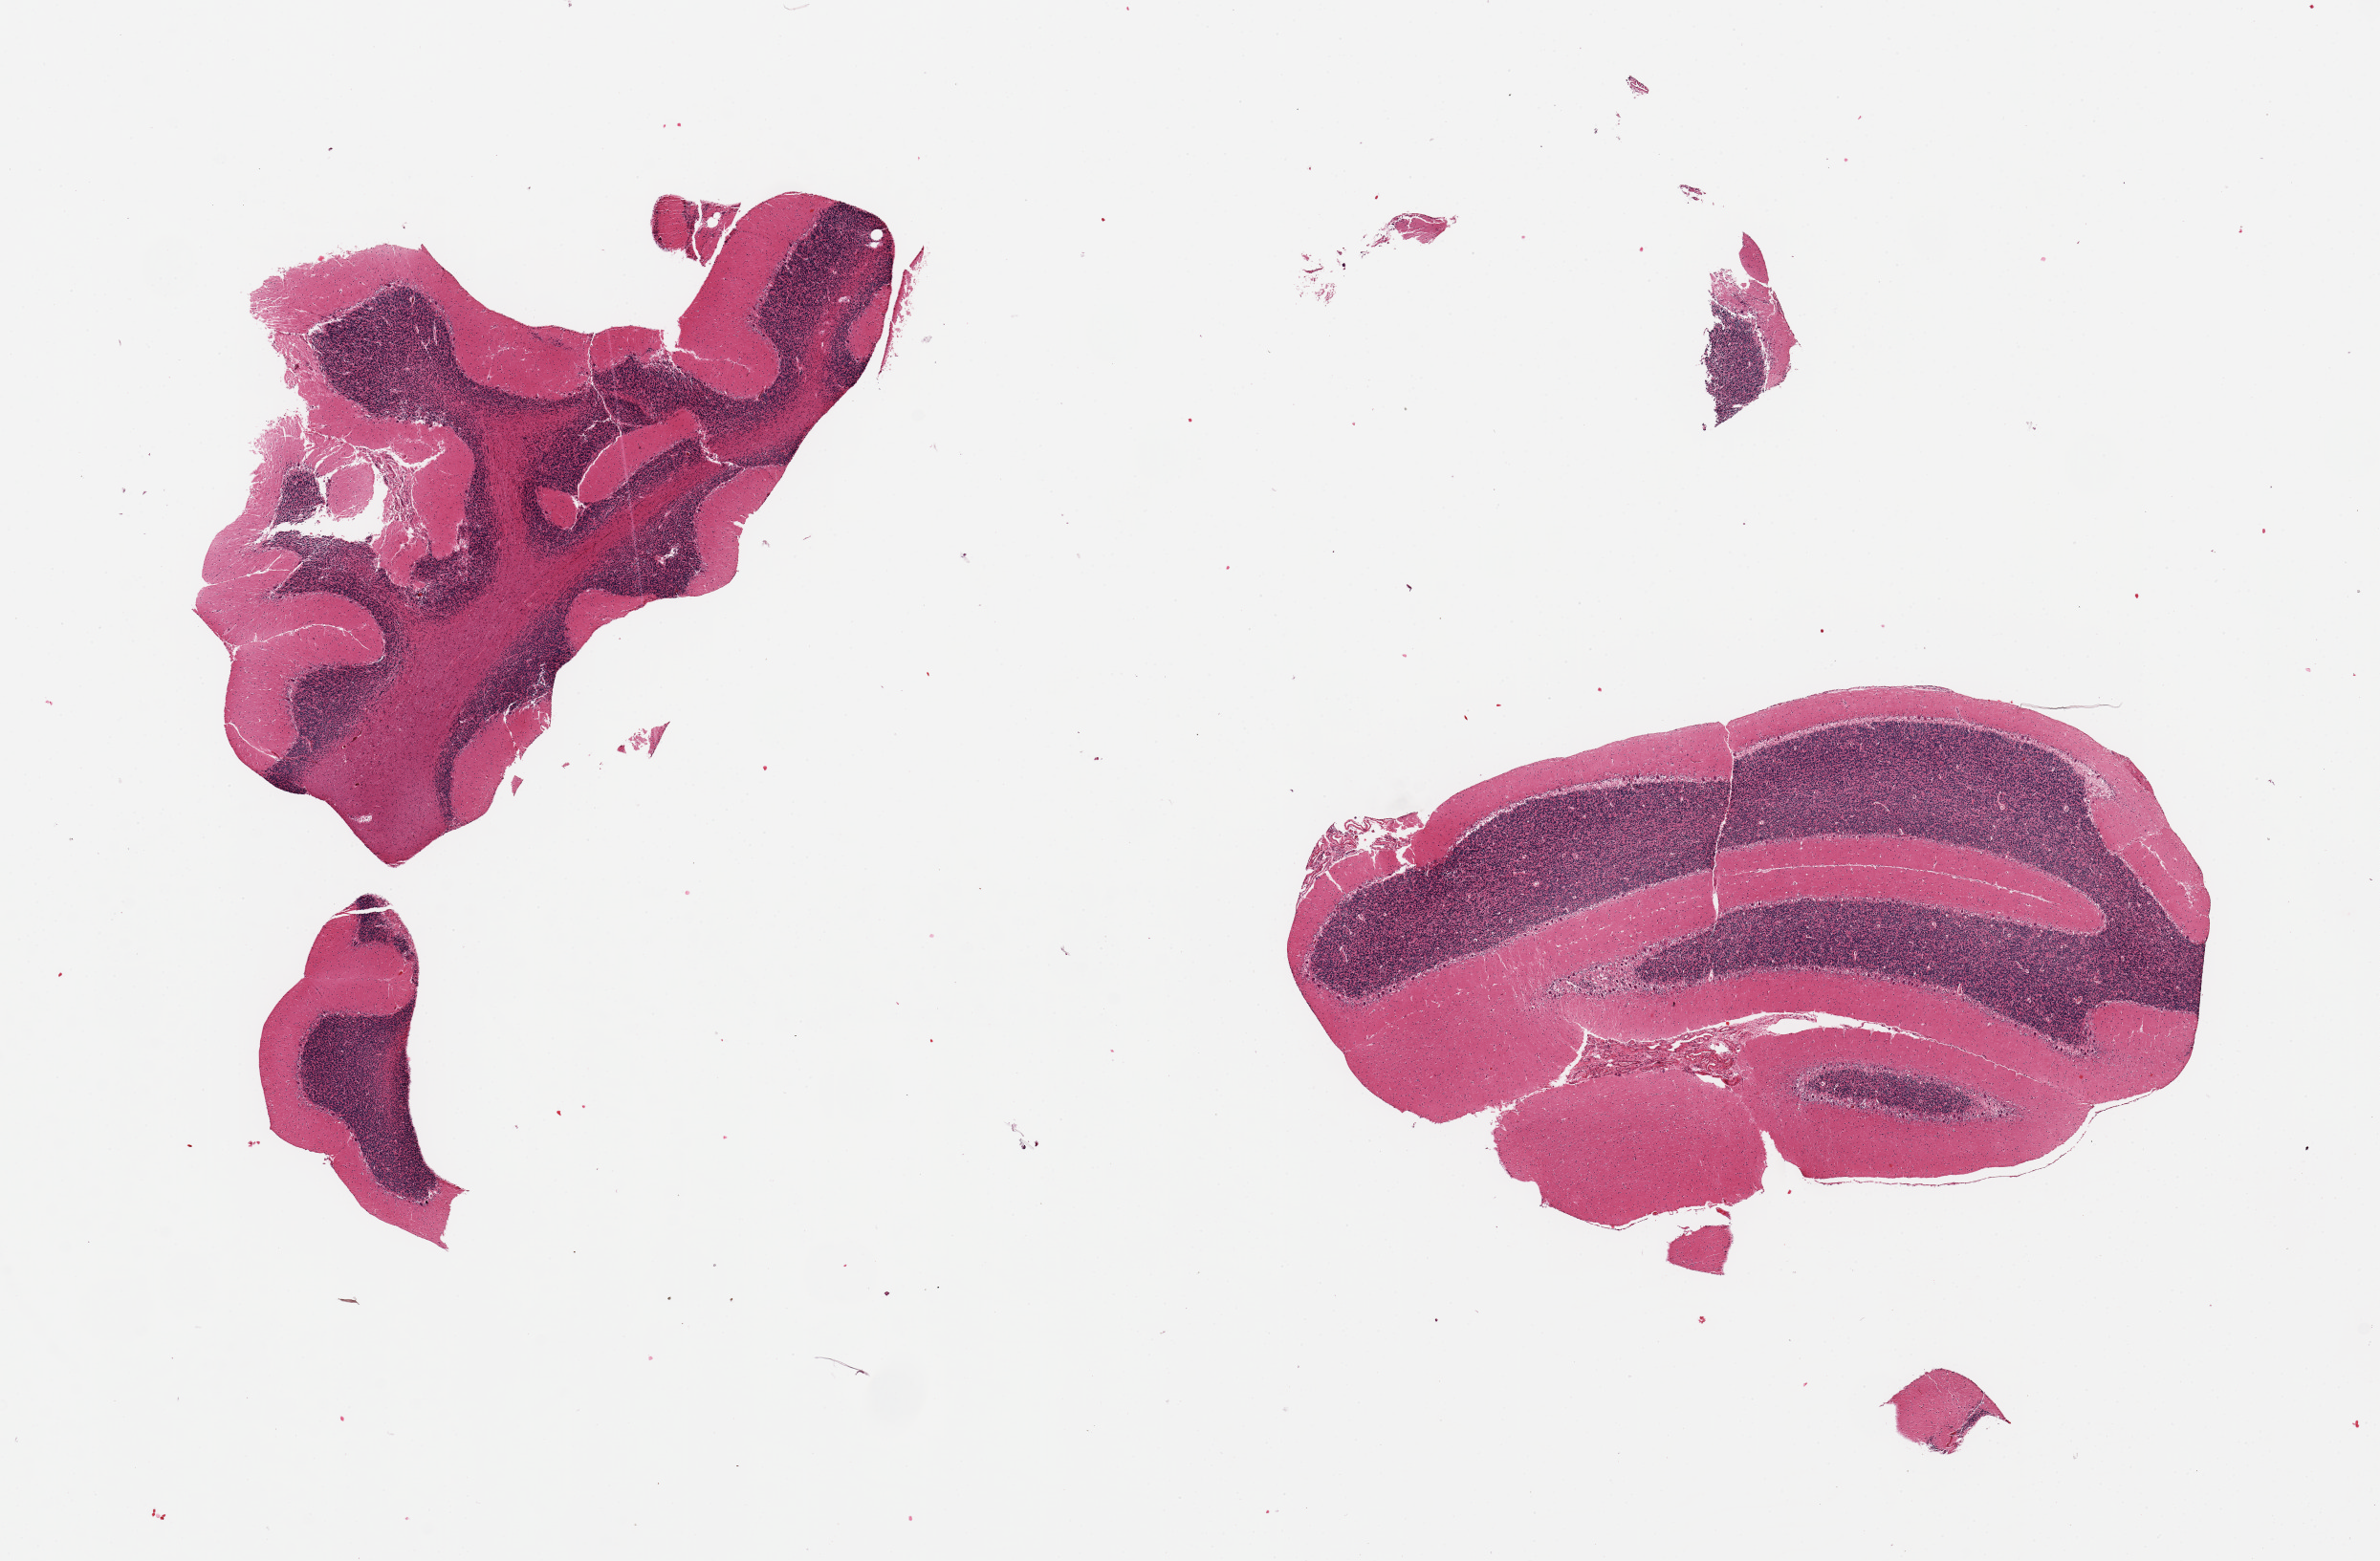
Haematoxylin and eosin whole-slide image, whole scanned area (about 19.7 x 12.9 mm) shown as a low-resolution overview, PAXgene-fixed, paraffin-embedded tissue, sampled site (target tissue): cerebellum, tissue donor sample. Donor sex: male.
Reviewer comment on this tissue sample: 2 pieces, no abnormalities noted.